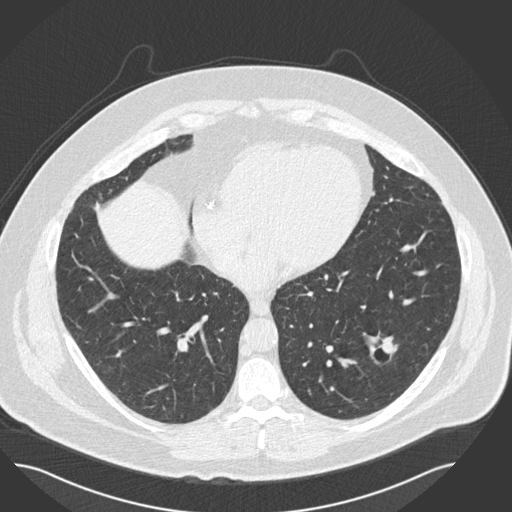
Low-dose screening chest CT, axial slice, second annual screen, lung window (W 1500 / L -600 HU), 2 mm slice thickness, slice 90 of 162 in the series, 512 × 512 image matrix, field of view 422 × 422 mm. Male, age 57 years at enrolment. Current smoker at enrolment.
Expert-annotated lung lesion, box from (x=349, y=325) to (x=415, y=376) px. Reader record for this screening exam (exam-level; its link to the box is not recorded): non-calcified nodule or mass ≥4 mm, left lower lobe, 19 × 15 mm, pre-existing on the prior screen: yes; interval growth: no. Lung cancer was diagnosed 434 days after this screen: squamous cell carcinoma, NOS, left lower lobe, moderately differentiated (G2), stage IA (AJCC 6th edition), 22 mm at pathology.